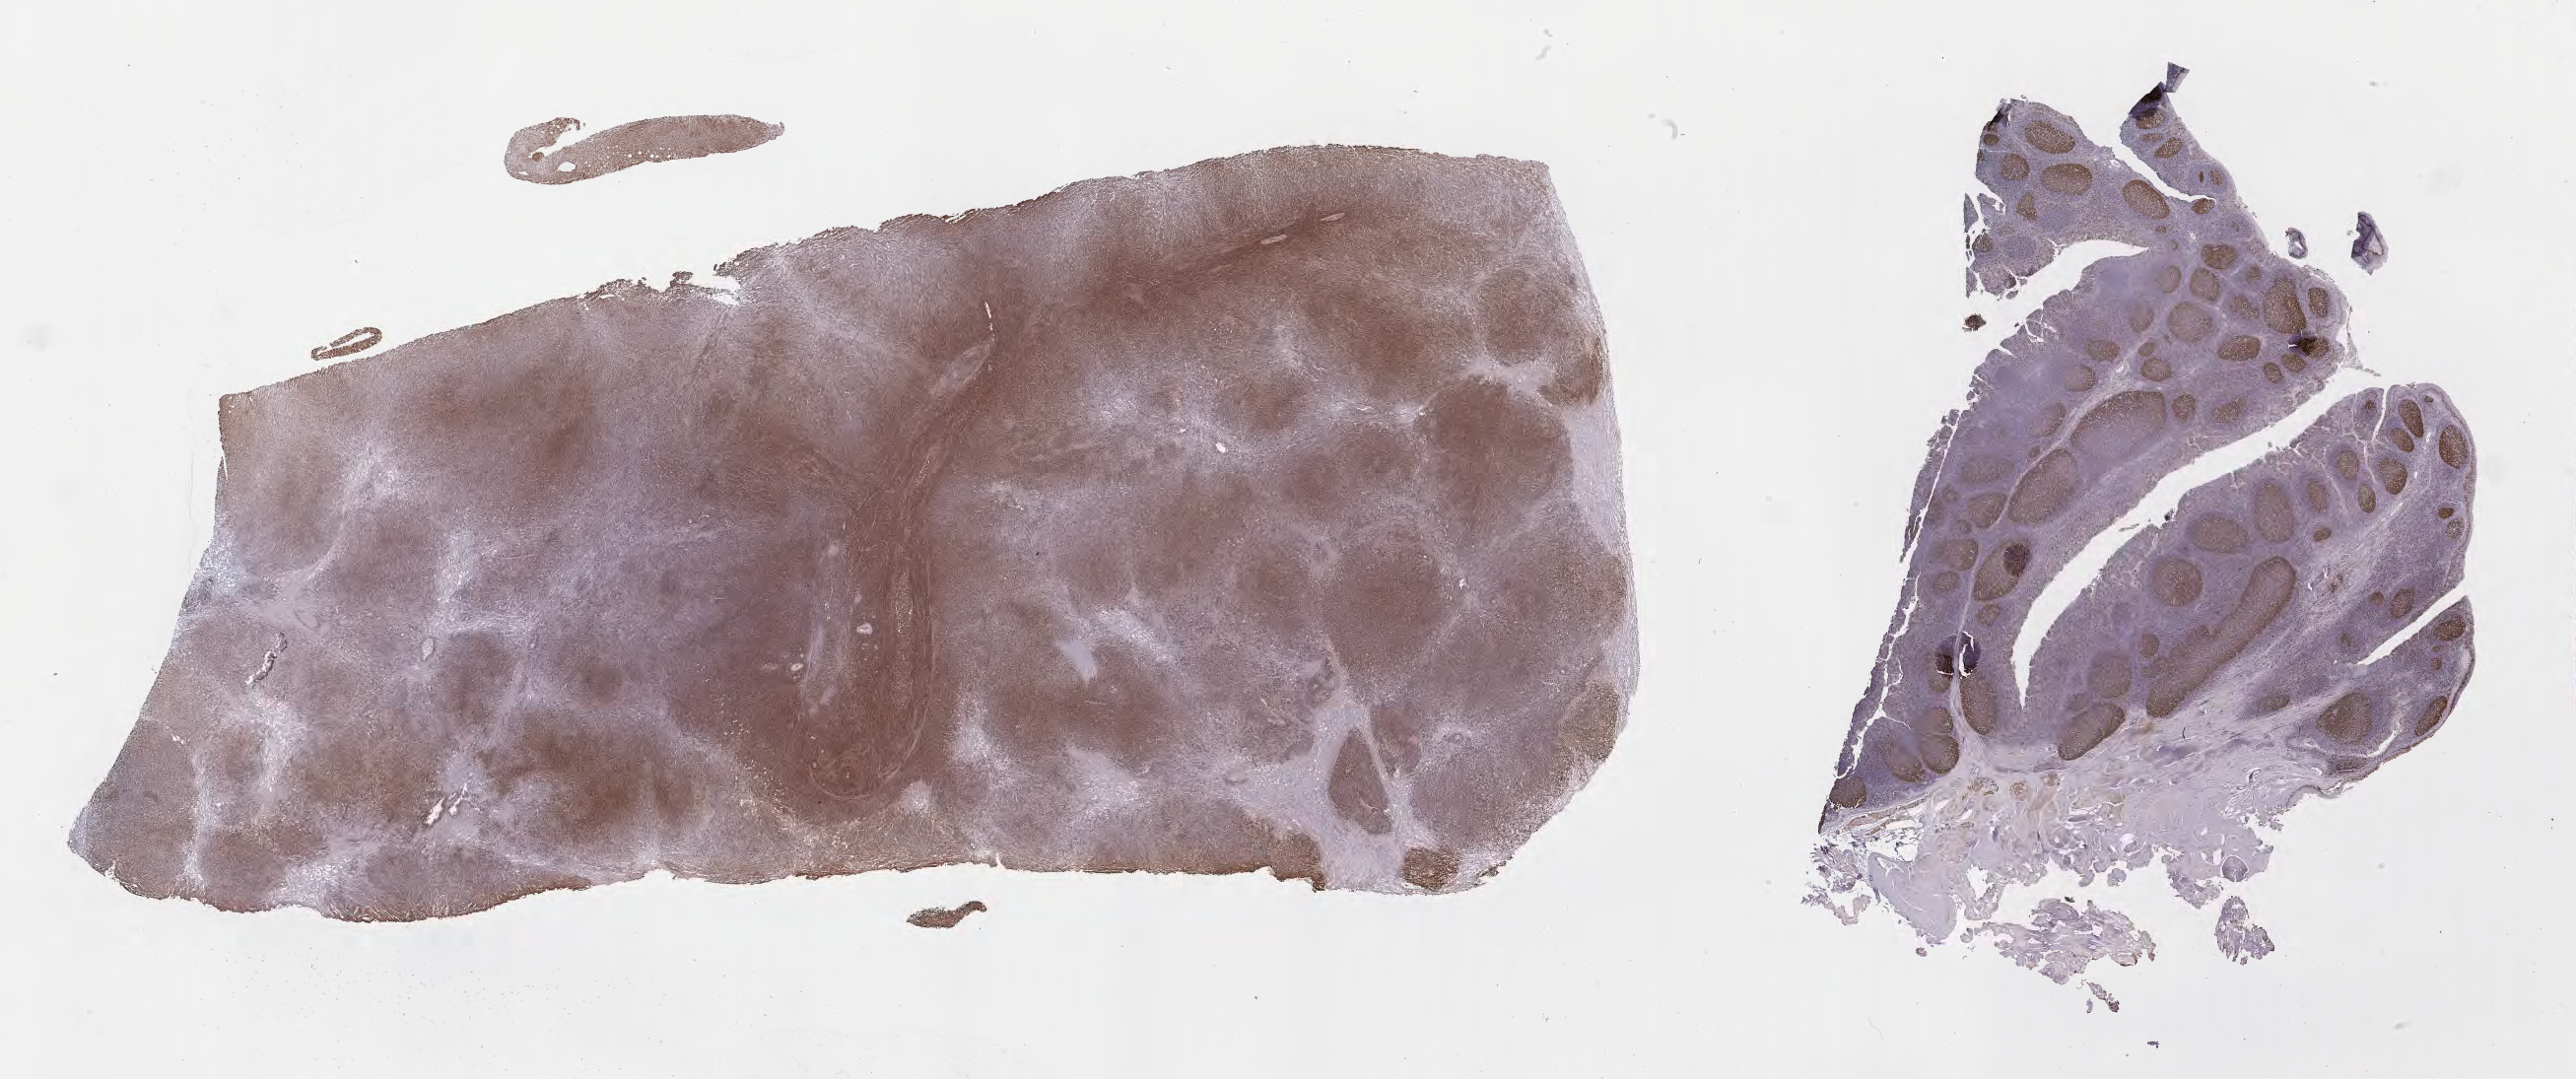
IHC for Ki-67, whole-slide image, shown as a low-resolution overview of the whole scanned area (about 42.3 x 17.7 mm). Tumor tissue. Patient: male, 39 years old.
Histologic diagnosis: Diffuse large B-cell lymphoma, NOS.